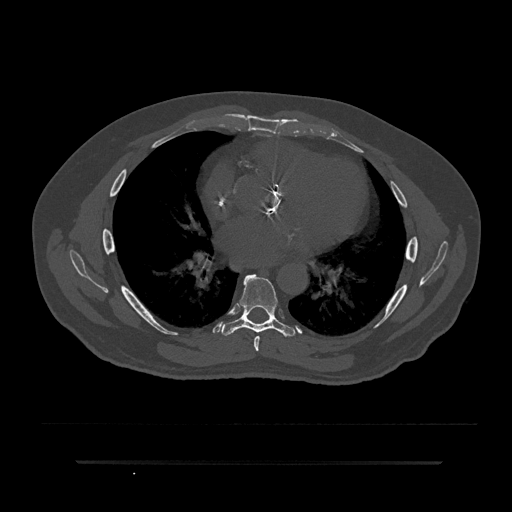
CT including the spine, one axial slice; slice 486 of 797 in the series (ordered by position); reconstruction kernel Br40s/3; 120 kVp; bone window (W 1800 / L 400 HU); 0.5 mm slice thickness; 512 × 512 image matrix, field of view 464 × 464 mm. Patient: male, 59 years. From the clinical record (not read from this slice): primary cancer: bile ducts; vertebrae with lytic lesions (as recorded): T10.
Structures marked on this image (semi-automatically segmented with operator editing):
- T6 vertebra: bounding box <254,336,260,352> (left, top, right, bottom; pixels)
- T7 vertebra: <221,274,295,337>